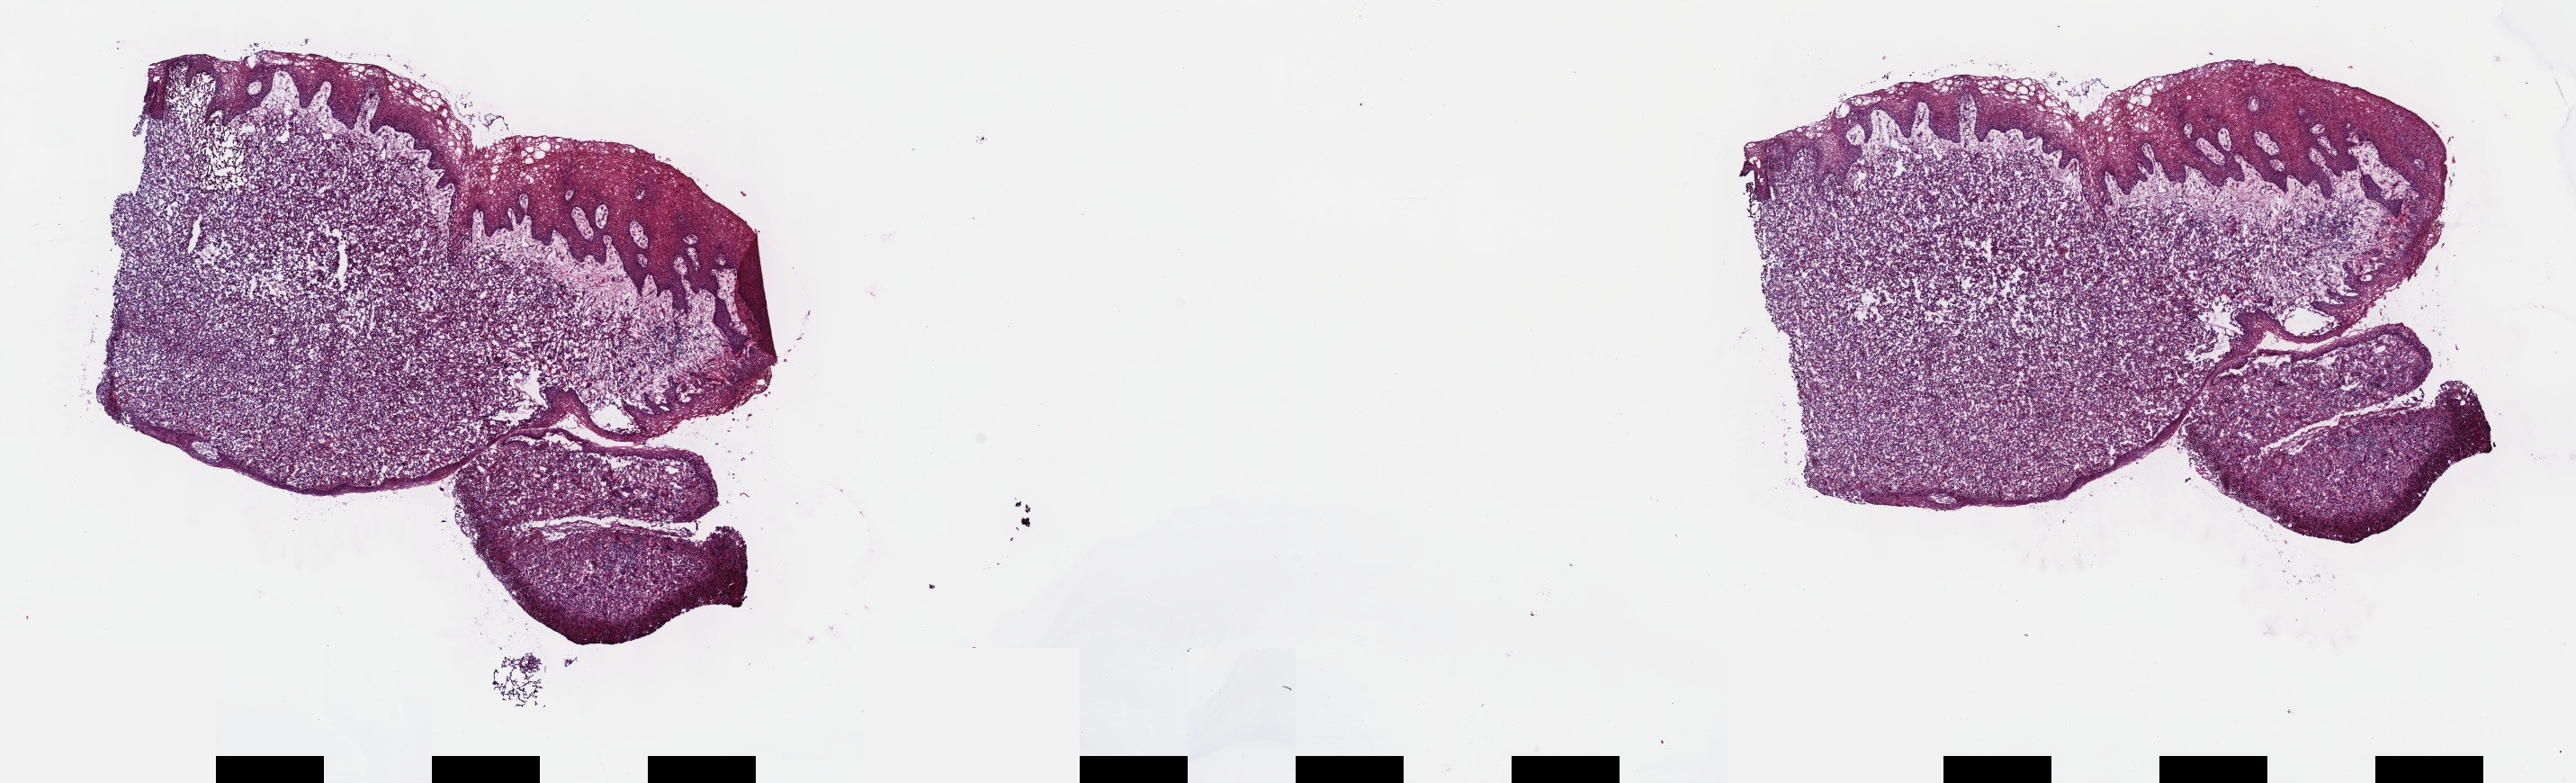
Digitized H&E tissue section (whole slide), whole scanned area (about 23.2 x 7.0 mm) shown as a low-resolution overview; frozen section from the top of the tissue portion; cervix, primary tumour sample. Female patient; age at initial diagnosis 48 years. Histologic grade: G3 (poorly differentiated). Slide review estimates, as recorded: tumour cells 80%, tumour nuclei 80%, normal cells 10%, stromal cells 5%, necrosis 5%. Inflammatory infiltration, as recorded: lymphocyte infiltration 4%, monocyte infiltration 0%, neutrophil infiltration 0%.
- pathologic diagnosis: Squamous cell carcinoma, NOS (cervix uteri)
- FIGO stage: IIIB